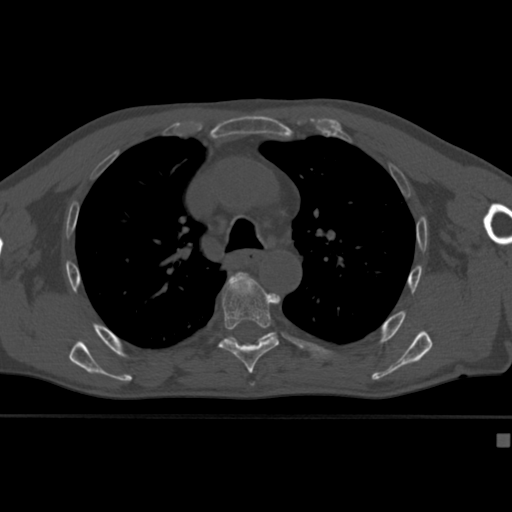
CT including the spine, one axial slice. Position 294 of 430 along the scan axis. Reconstruction kernel Br40s. Bone window (W 1800 / L 400 HU). 1.5 mm slice thickness. 512 × 512 image matrix, field of view 337 × 337 mm. Male patient, age 64 years. Case-level facts recorded for this patient, not image findings: primary cancer: uterus; vertebrae with lytic lesions (as recorded): T1, T4, T5, T7, L5.
Outlined on this slice (semi-automatically segmented with operator editing):
- T5 vertebra: box from (x=231, y=272) to (x=249, y=280) px
- T6 vertebra: (x=218, y=275)–(x=280, y=374)
- T7 vertebra: (x=229, y=332)–(x=273, y=341)